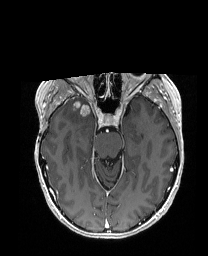
Brain MRI from a brain-tumour surgery series, one axial slice. Slice 114 of 192 in the series (ordered by position). T1-weighted post-contrast. 1 mm slice thickness. 208 × 256 image matrix, field of view 203 × 250 mm. From the clinical record (not read from this slice): histopathology: Metastatic Carcinoma from Breast primary; tumour location: Right Frontal.
Outlined on this slice (expert manual segmentation):
- tumour: bounding box [x1, y1, x2, y2] px = [78, 100, 96, 114]